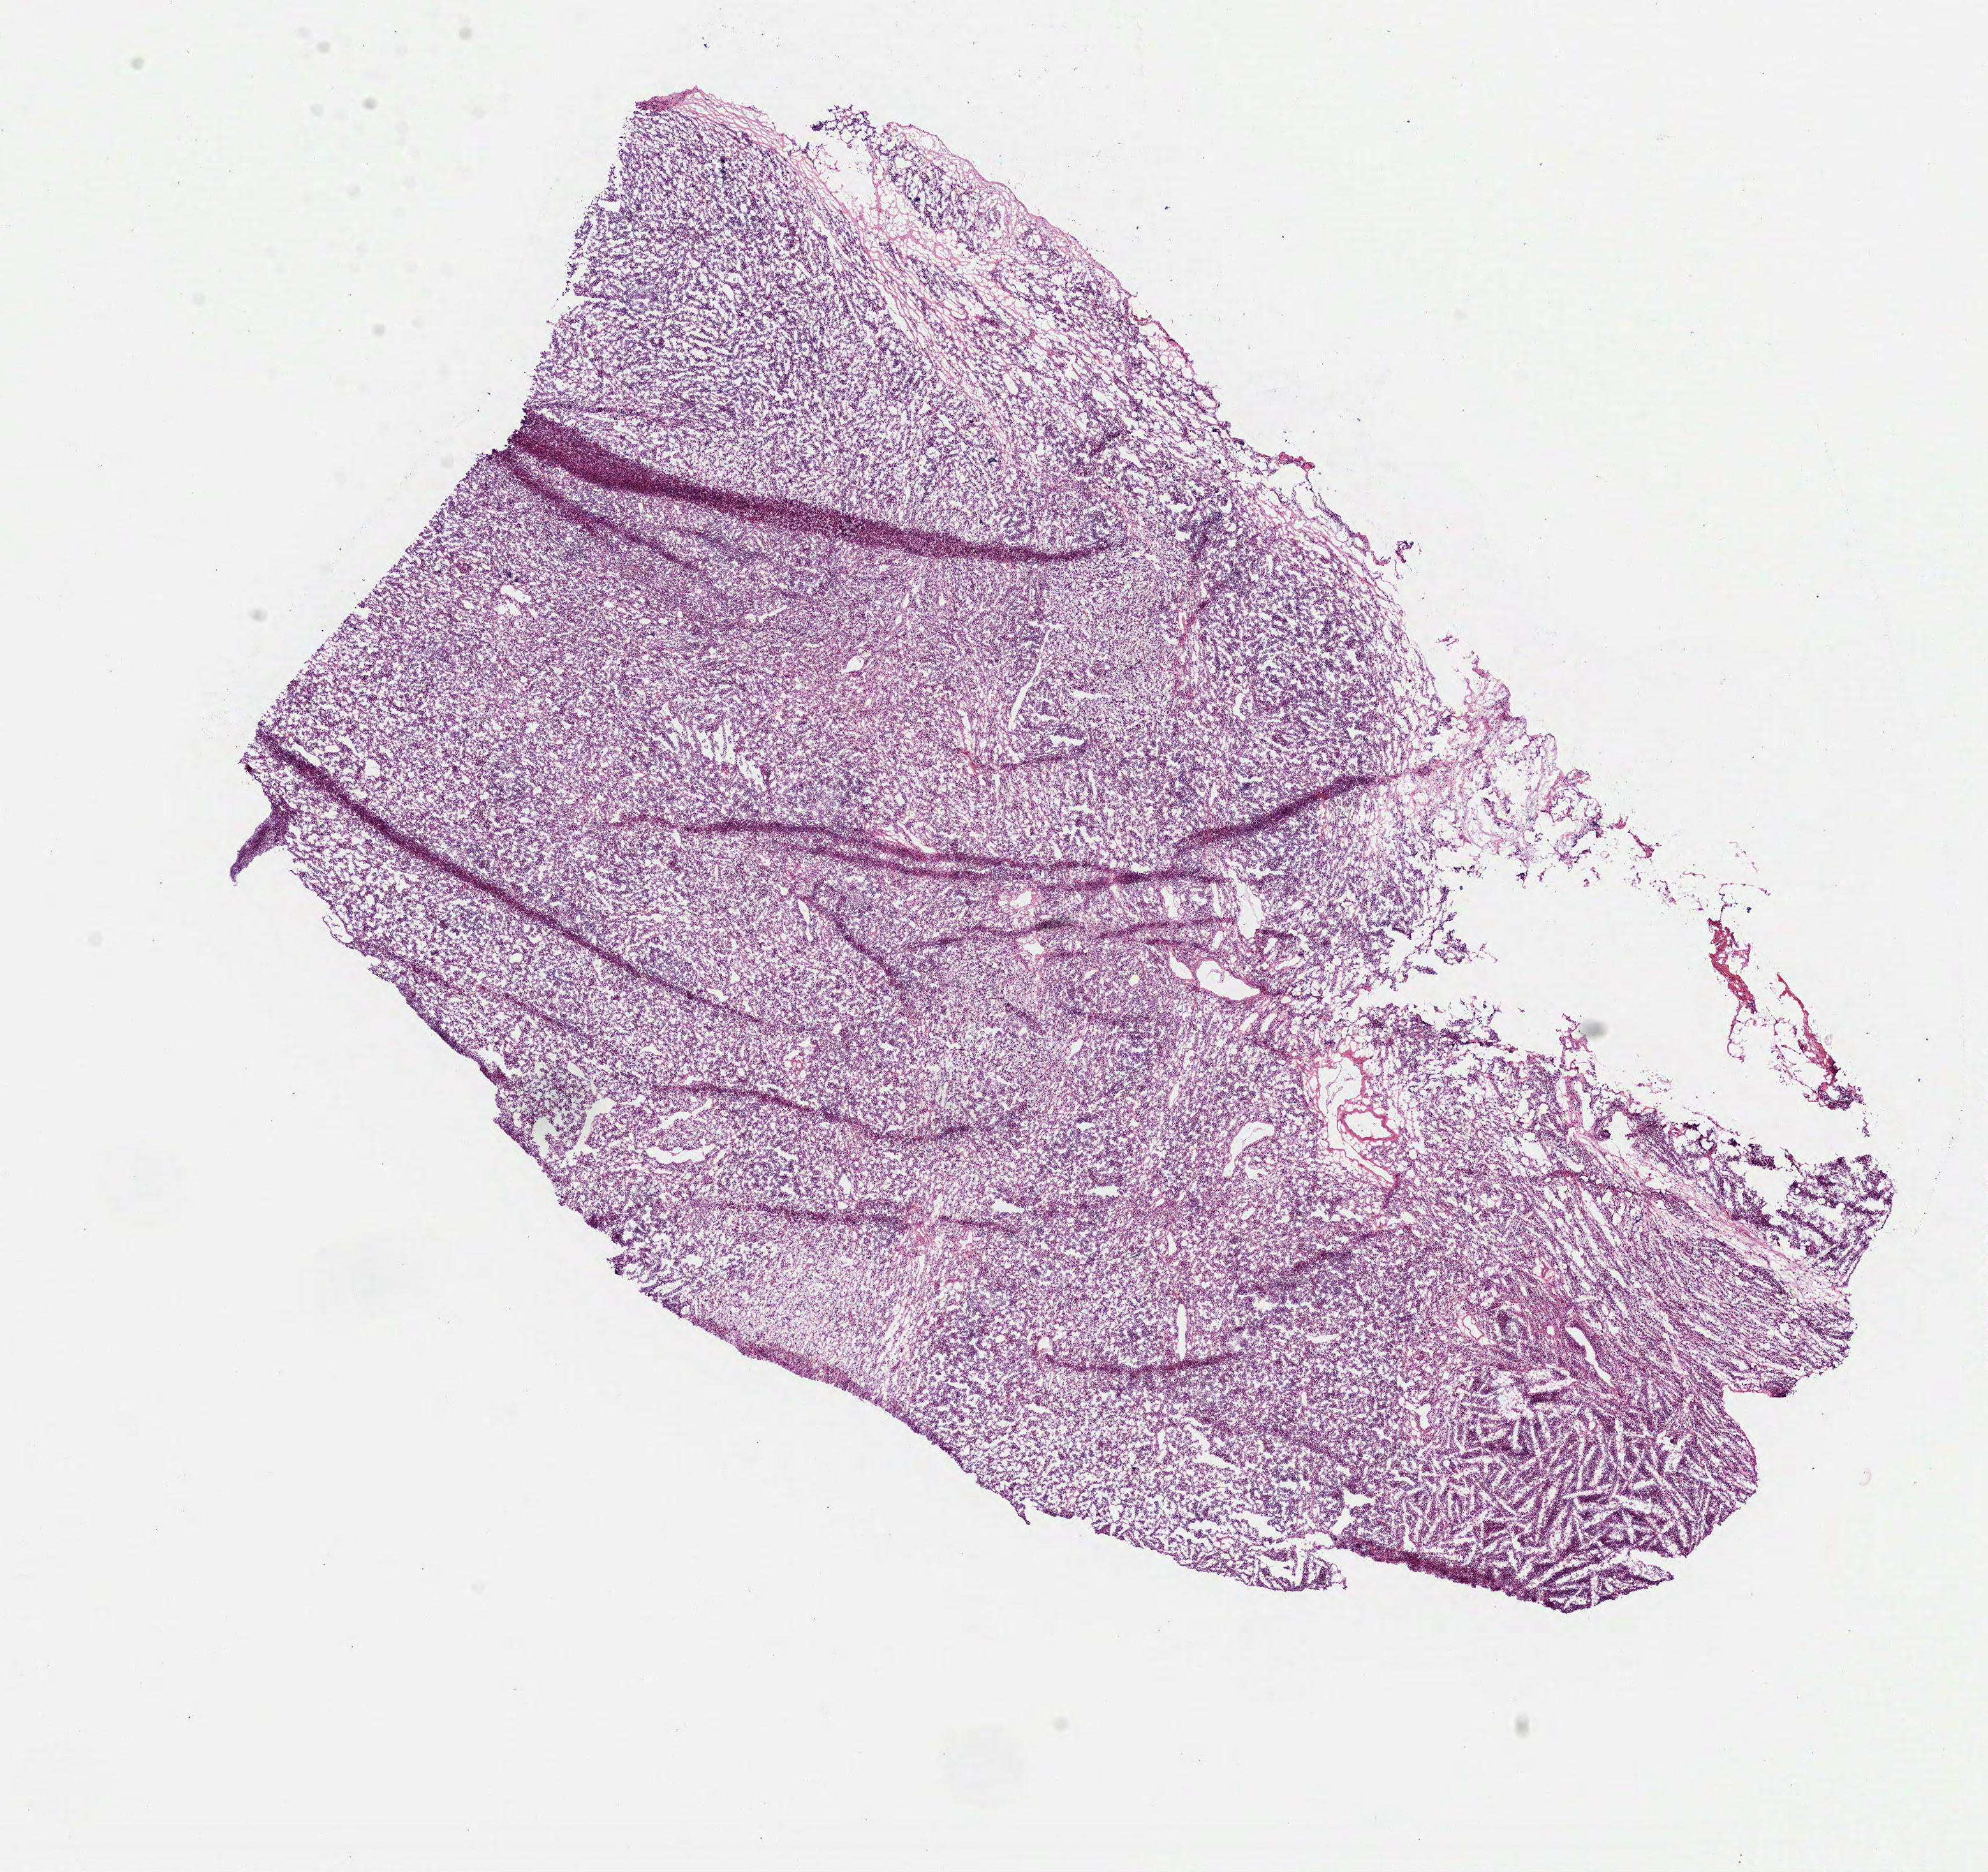
Digitized Hematoxylin and eosin (H&E) stained tissue section (whole slide) — low-resolution overview of the scanned area, about 12.6 x 11.8 mm (from a 40x scan), frozen section from the top of the tissue portion, primary tumour sample from the stomach. Male, age 59 years at initial diagnosis. Histologic grade: G3 (poorly differentiated). Slide review estimates, as recorded: tumour cells 90%, tumour nuclei 70%, normal cells 0%, stromal cells 10%, necrosis 0%. Inflammatory infiltration, as recorded: lymphocyte infiltration 20%, monocyte infiltration 0%, neutrophil infiltration 0%.
Lymph nodes positive (case pathology): 21 of 24 examined. Diagnosis: Carcinoma, diffuse type (cardia, NOS).